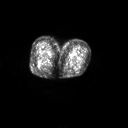
FDG PET of an extremity soft-tissue mass (from a PET/CT study), one axial slice; 128 × 128 image matrix, field of view 700 × 700 mm. Female patient, age 70 years. Case-level facts recorded for this patient, not image findings: histological type: synovial sarcoma; grade: intermediate; site of the primary tumour: right buttock.
Structures marked on this image (expert contour drawn on MRI and transferred to this co-registered scan by the dataset authors):
- gross tumour volume including surrounding oedema: bounding box <36,65,39,68> (left, top, right, bottom; pixels)